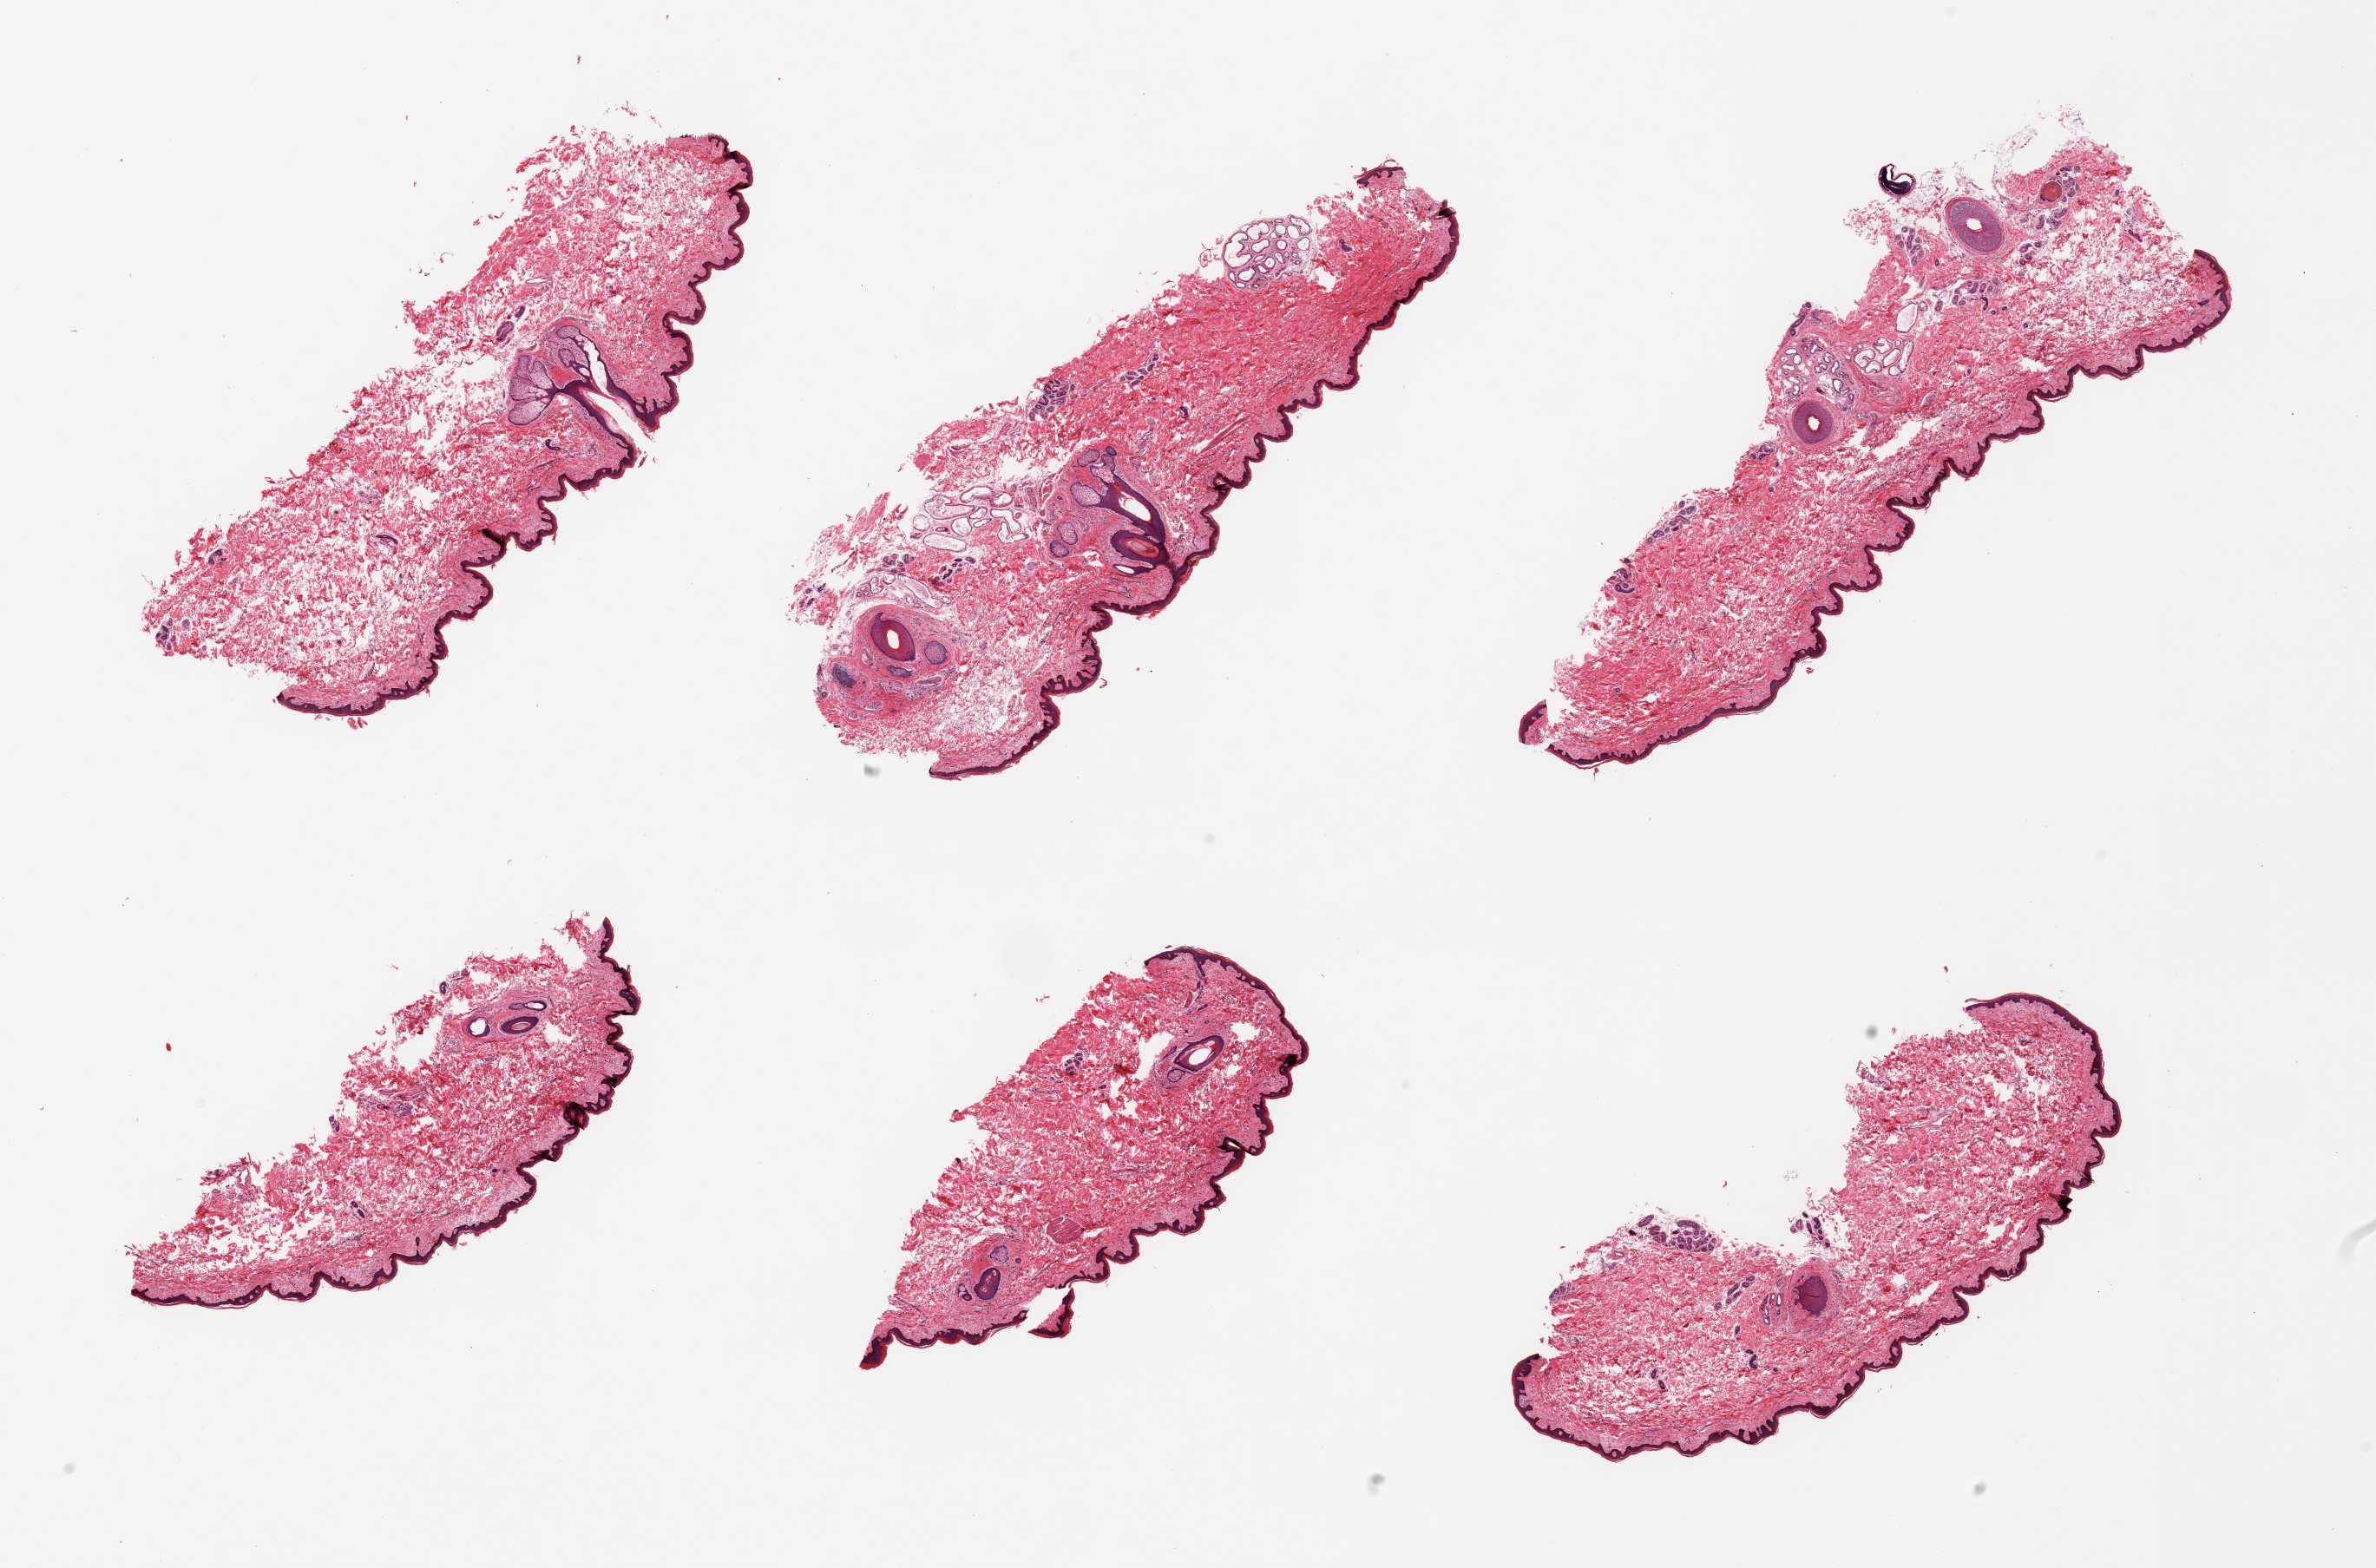
Whole-slide image, haematoxylin and eosin stain — a low-resolution overview of the entire scanned area, about 21.7 x 14.3 mm; PAXgene-fixed paraffin-embedded (PFPE) section; section of skin of suprapubic region (target tissue); tissue donor sample. Donor sex: male.
- reviewer comment on this tissue sample: 6 pieces; well trimmed